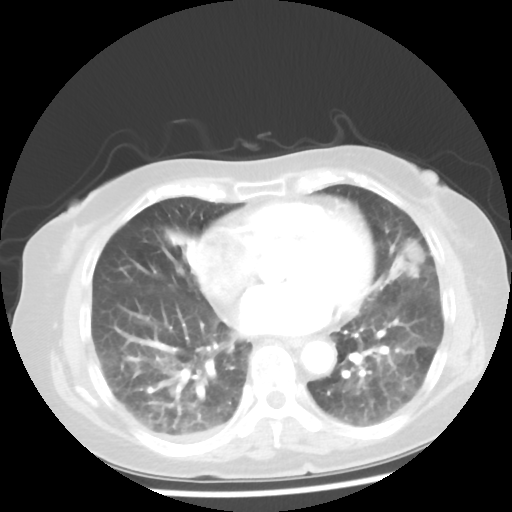
Chest CT, one axial slice; position 19 of 50 along the scan axis; 100 kVp; lung window (W 1500 / L -600 HU); 5 mm slice thickness; 512 × 512 image matrix. Patient: female, 77 years. Case-level facts recorded for this patient, not image findings: clinical TNM (as recorded): T2 N3 M1a.
Structures marked on this image (rectangle marked by the reading radiologist):
- lung tumour (recorded histology: adenocarcinoma): bounding box (x1, y1, x2, y2) in pixels: (388, 232, 429, 285)